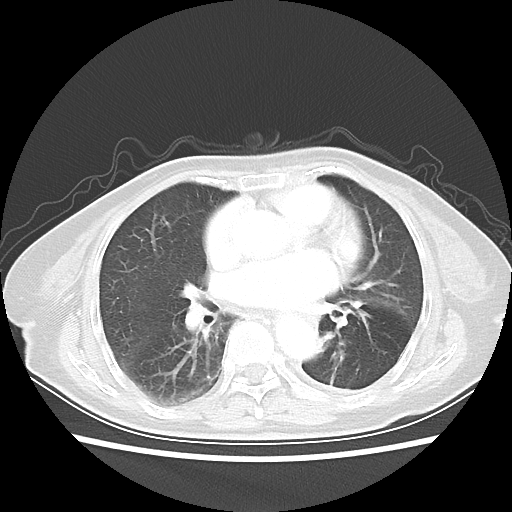
Chest CT, one axial slice. Slice 24 of 50 in the series (ordered by position). 80 kVp. Lung window (W 1500 / L -600 HU). 512 × 512 image matrix, field of view 335 × 335 mm. Female patient, age 81 years. From the clinical record (not read from this slice): clinical TNM (as recorded): T2 N0 M1a.
Outlined on this slice (rectangle marked by the reading radiologist):
- lung tumour (recorded histology: squamous cell carcinoma): bounding box <311,317,341,378> (left, top, right, bottom; pixels)